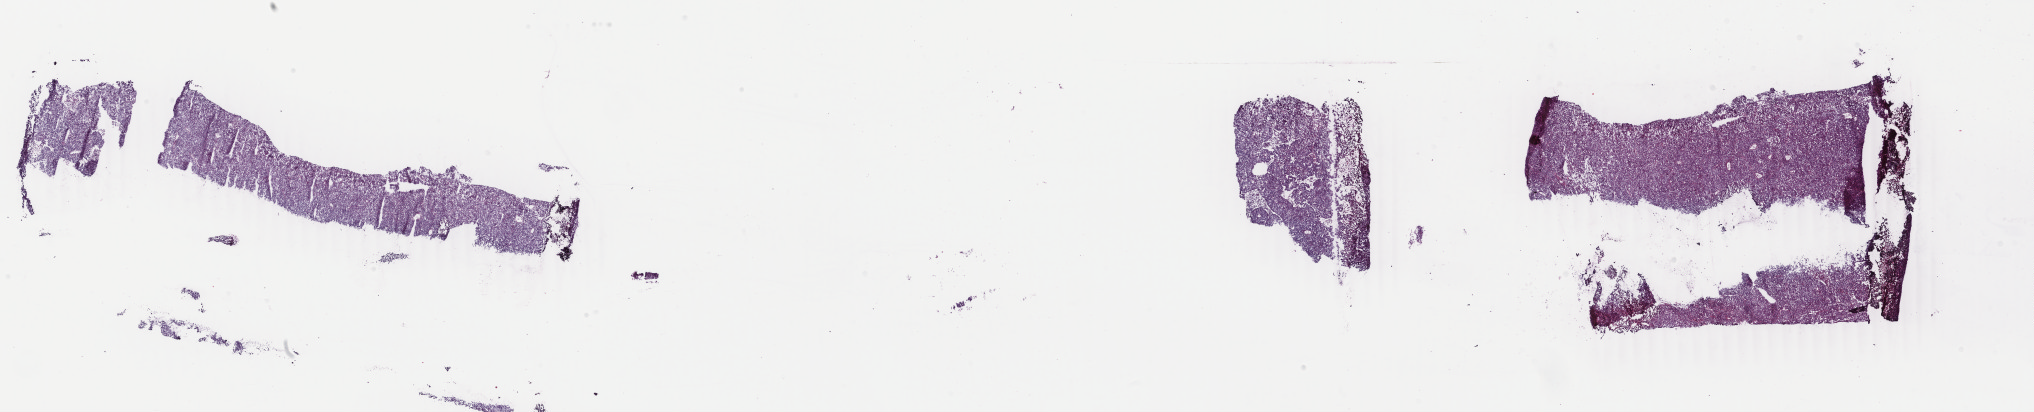
Digitized H&E tissue section (whole slide) — shown as a low-resolution overview of the whole scanned area (about 32.4 x 6.6 mm, slide scanned at 40x). Frozen section from the top of the tissue portion. Primary tumour sample from the uterus. Patient: female, age at initial diagnosis 47 years. Histologic grade: high grade. Slide review estimates, as recorded: tumour cells 70%, tumour nuclei 90%, normal cells 0%, stromal cells 10%, necrosis 20%. Infiltration values recorded for this section: lymphocyte infiltration 30%, monocyte infiltration 0%, neutrophil infiltration 10%.
Diagnosis: Serous cystadenocarcinoma, NOS (endometrium). FIGO stage: IA.